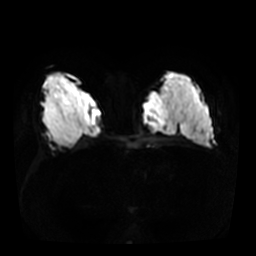
Breast MRI, one axial slice; position 17 of 36 along the scan axis; diffusion-weighted series; image 2 of 4 stored at this slice position (different b-values; order by instance number); 3 T; 256 × 256 image matrix, field of view 340 × 340 mm. Female patient.
Outlined on this slice (manually delineated by an expert):
- tumour on diffusion-weighted imaging: bounding box <162,87,181,135> (left, top, right, bottom; pixels)